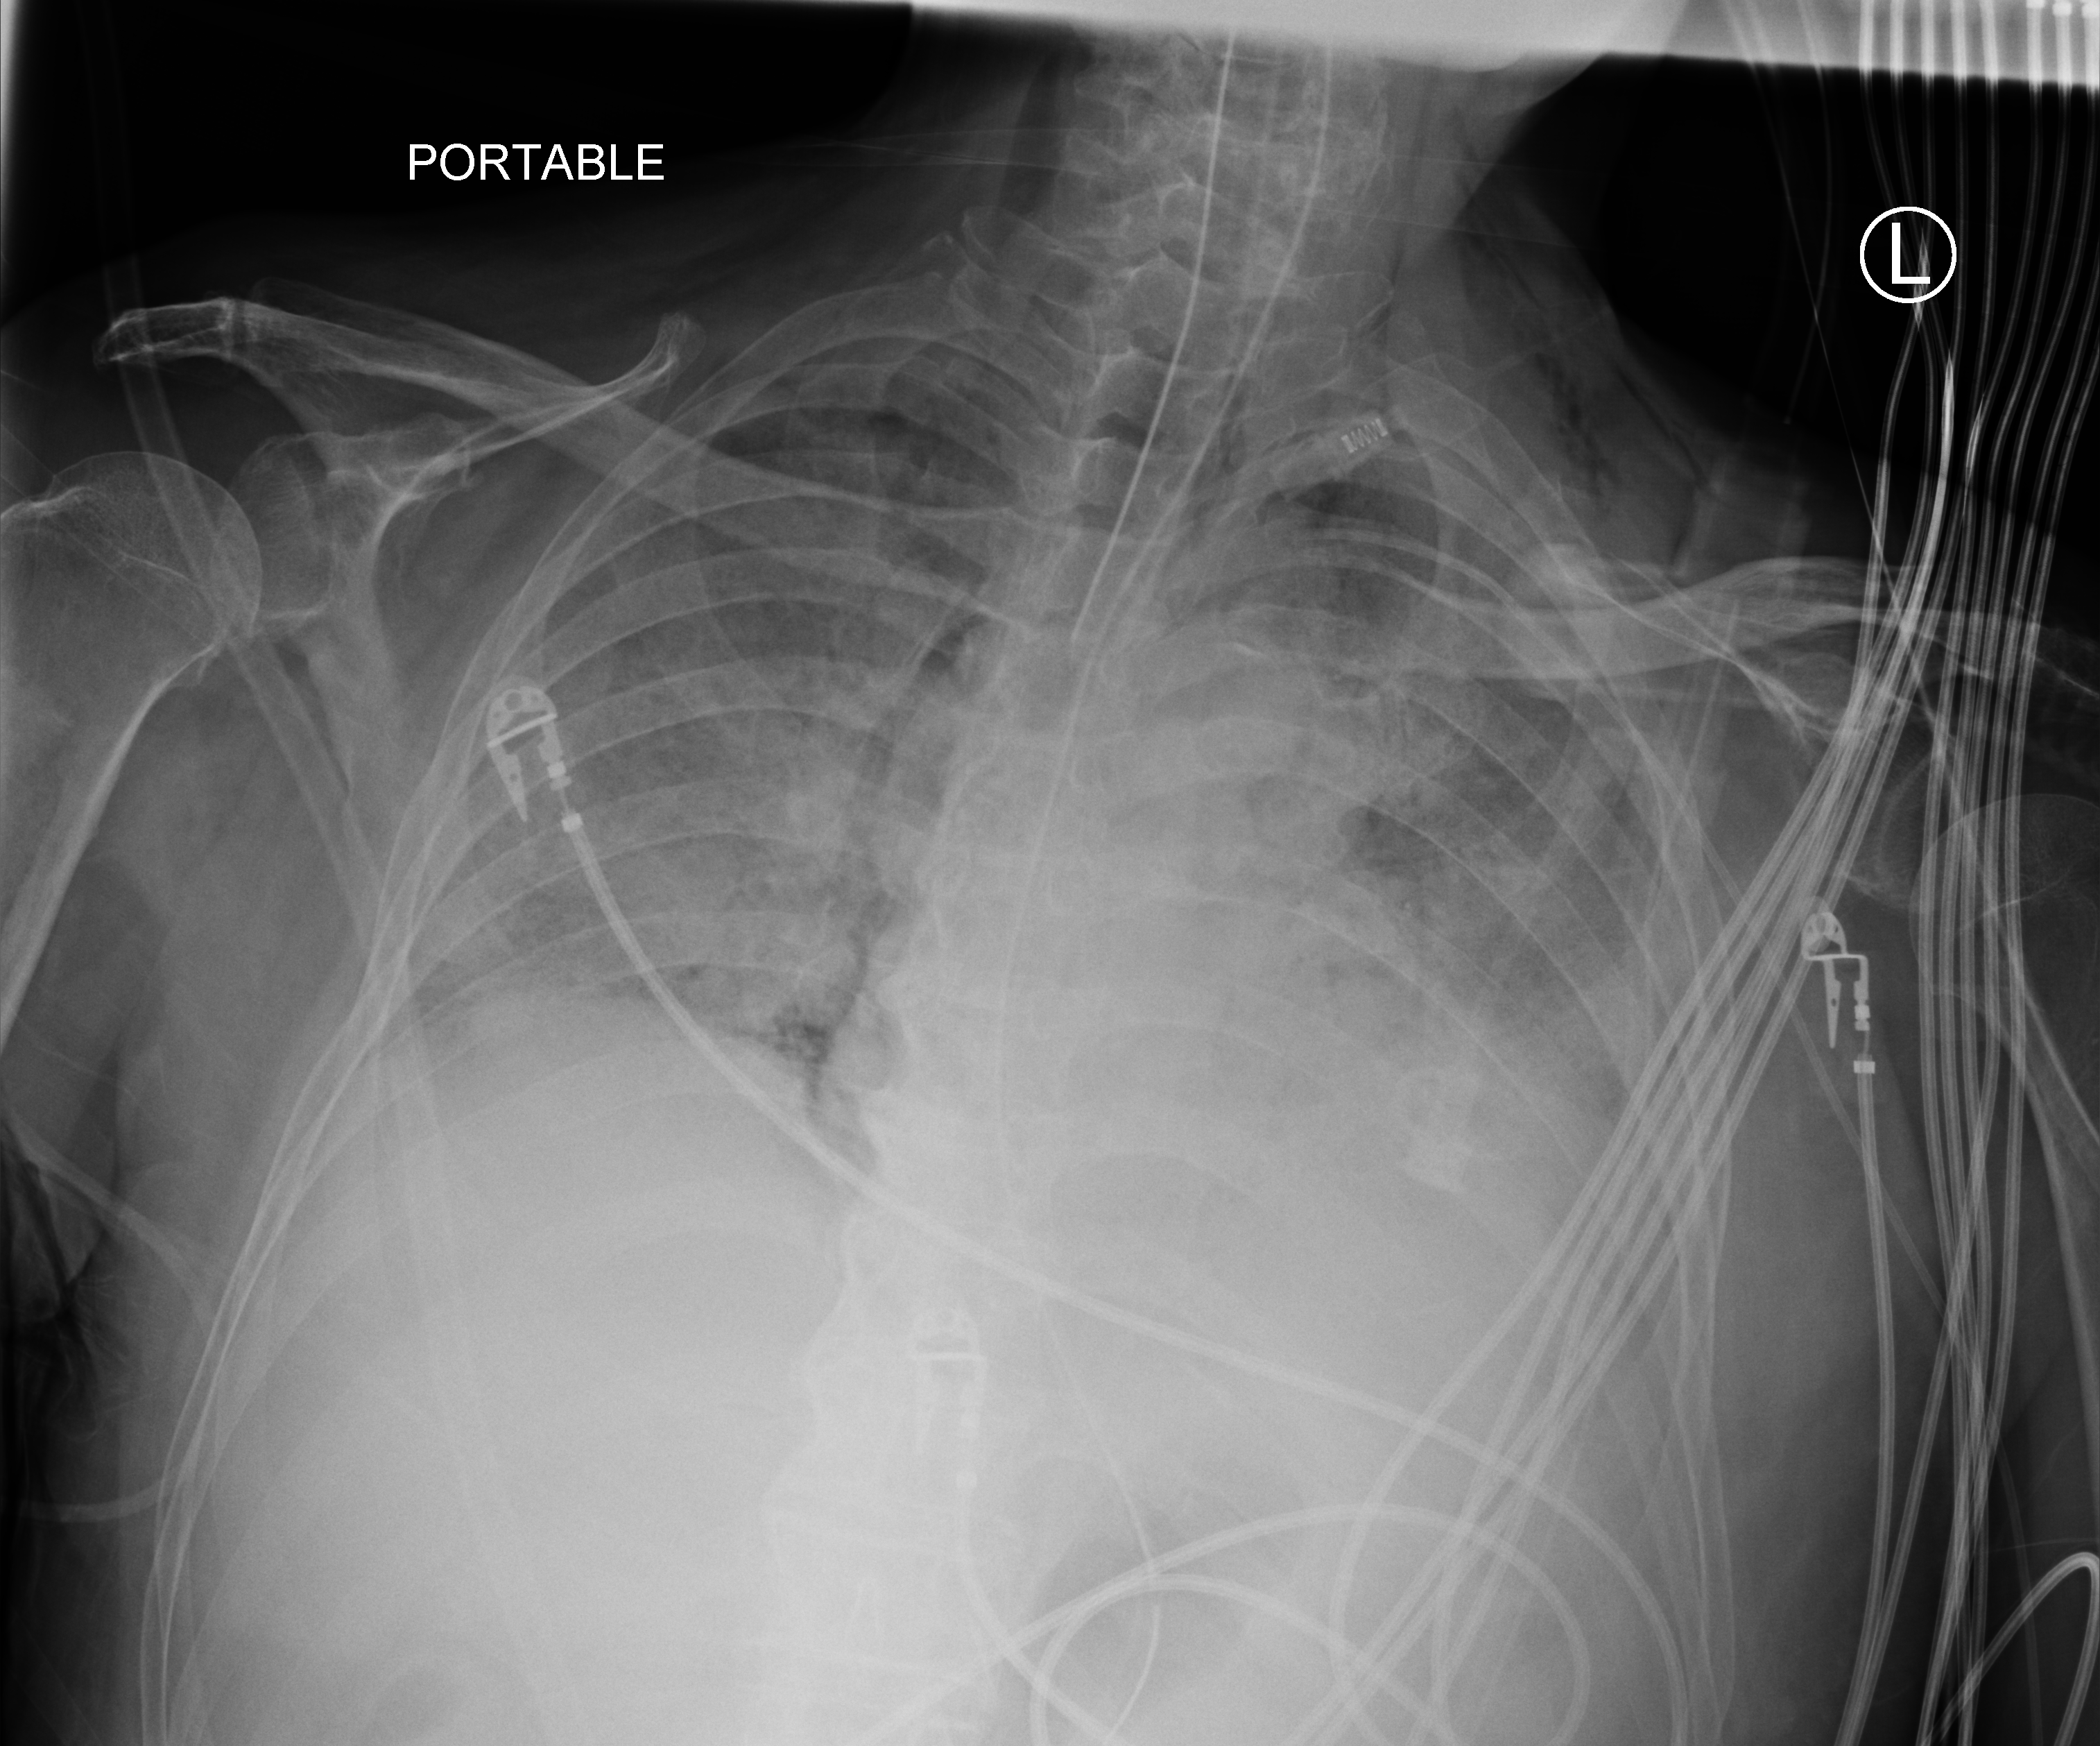
Chest X-ray (portable); anteroposterior (AP) projection. Patient hospitalised with COVID-19; male, aged 75–90 years.
Admission-level facts for this patient (not findings on this image; timing relative to this image not recorded): COPD (admission record): no; mechanically ventilated during this hospital stay: yes.